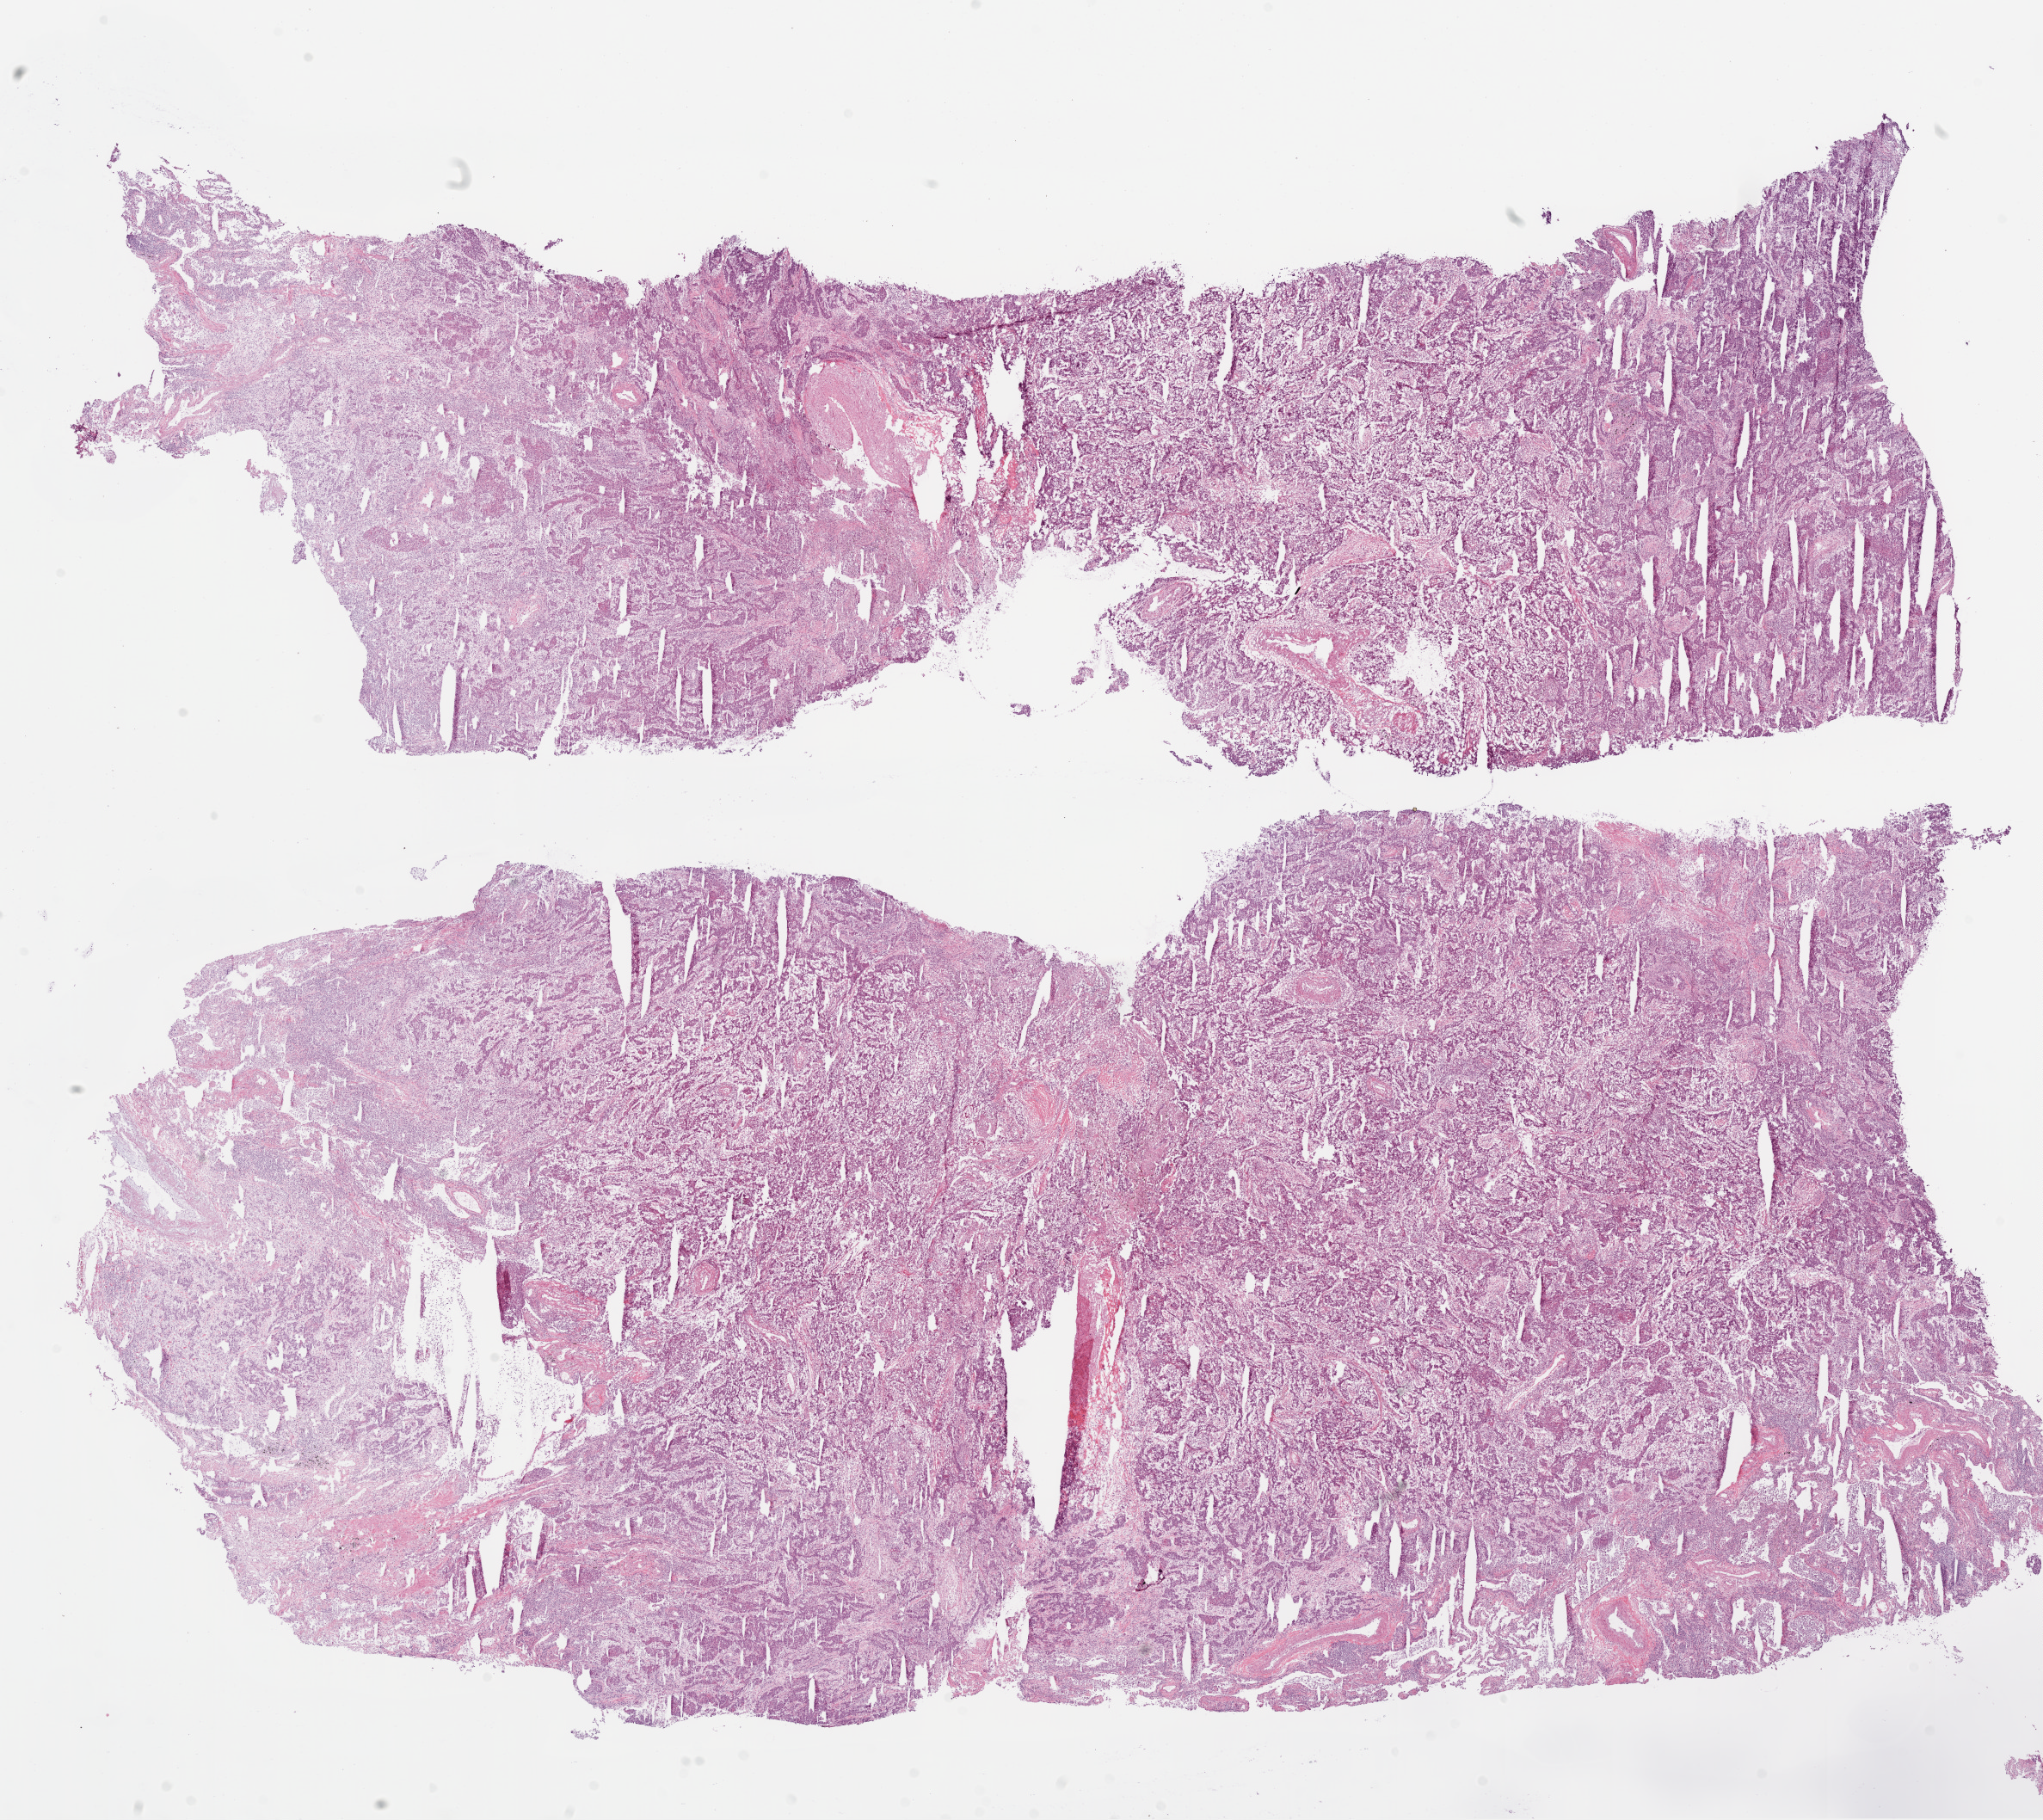
Hematoxylin and eosin (H&E) stained whole-slide image, low-resolution overview of the scanned area, about 19.1 x 17.0 mm (slide scanned at 20x), frozen section from the top of the tissue portion, sample: primary tumour, lung. Female patient; age at initial diagnosis 72 years. Composition of this section per pathologist review: tumour cells 75%, tumour nuclei 75%.
Diagnosis: Squamous cell carcinoma, NOS (lower lobe, lung).